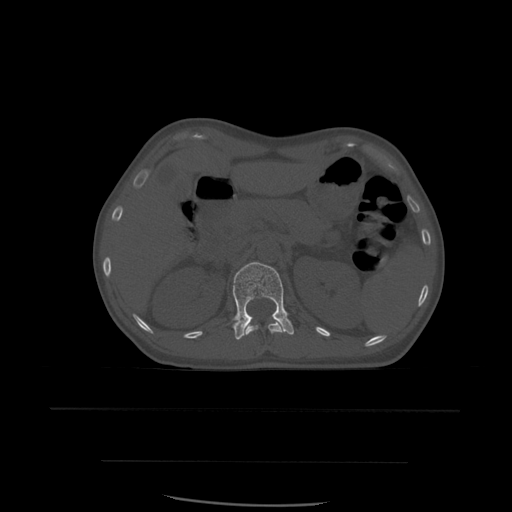
CT including the spine, one axial slice. Slice 256 of 574 in the series (ordered by position). Bone window (W 1800 / L 400 HU). 1.25 mm slice thickness. 512 × 512 image matrix. Patient age 48 years. From the clinical record (not read from this slice): primary cancer: lung.
Annotated regions visible in this slice (semi-automatic segmentation, software-assisted and operator-edited):
- L1 vertebra: bounding box [x1, y1, x2, y2] px = [233, 262, 295, 340]
- T12 vertebra: [245, 319, 285, 335]